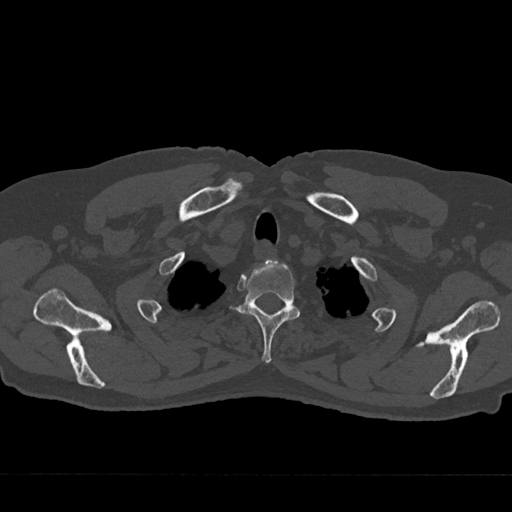
CT including the spine, one axial slice. Position 613 of 797 along the scan axis. Reconstruction kernel Br40s/3. Bone window (W 1800 / L 400 HU). 512 × 512 image matrix, field of view 377 × 377 mm. Male patient, age 75 years. From the clinical record (not read from this slice): primary cancer: renal; vertebrae with lytic lesions (as recorded): T4.
Annotated regions visible in this slice (semi-automatically segmented with operator editing):
- T2 vertebra: bounding box (x1, y1, x2, y2) in pixels: (232, 259, 300, 363)